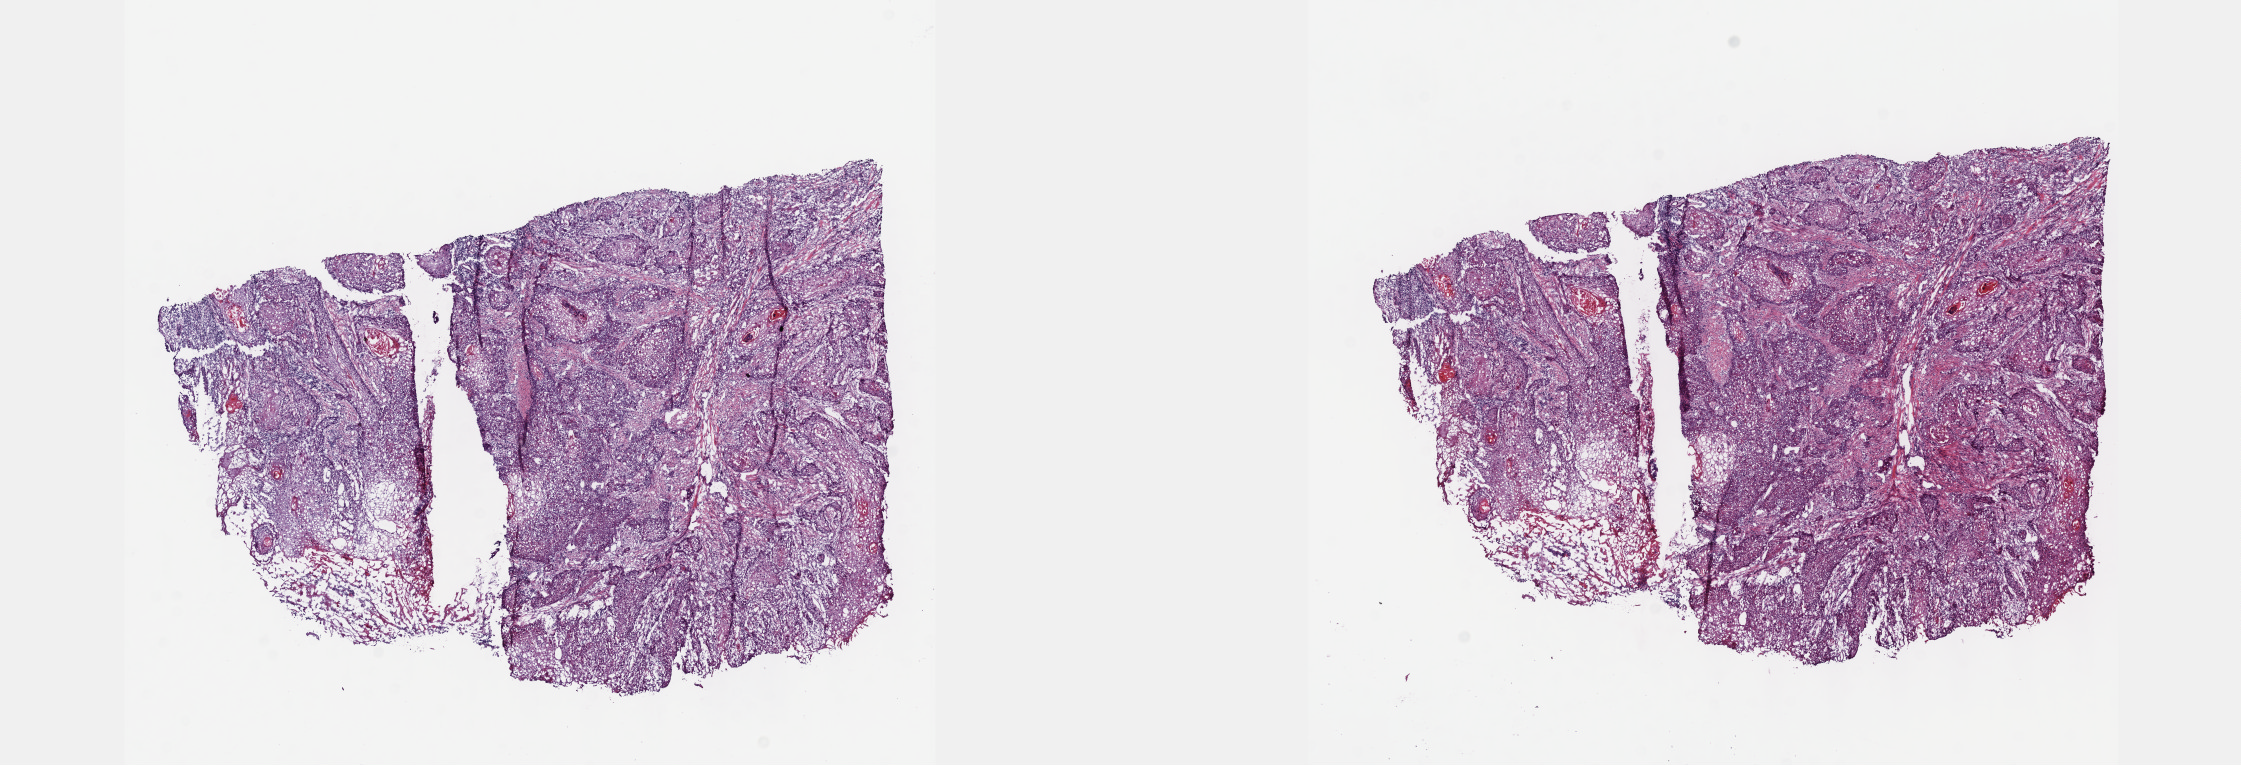
Digitized Hematoxylin and eosin (H&E) stained tissue section (whole slide) — whole scanned area (about 18.1 x 6.2 mm) shown as a low-resolution overview, frozen section from the top of the tissue portion, sample: primary tumour, head and neck. Patient: male, age at initial diagnosis 68 years. Histologic grade: G2 (moderately differentiated). Pathologist review of this section (percent, as recorded): tumour cells 50%, tumour nuclei 70%, normal cells 0%, stromal cells 50%, necrosis 0%. Inflammatory infiltration, as recorded: lymphocyte infiltration 20%, monocyte infiltration 0%, neutrophil infiltration 0%.
AJCC pathologic stage: IVA. TNM: T4a N0 M0. Diagnosis: Squamous cell carcinoma, NOS.